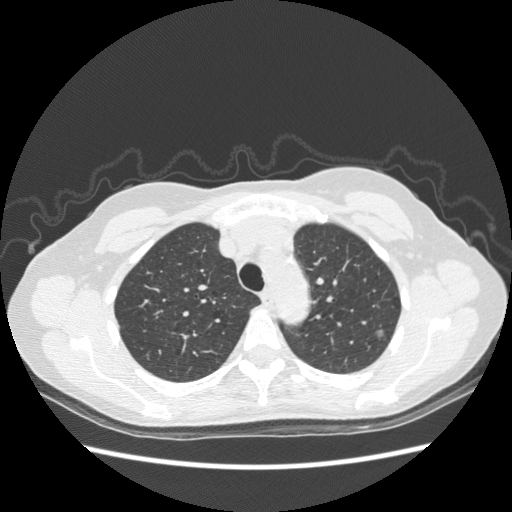
Low-dose screening chest CT, axial slice. First (baseline) screen. Lung window (W 1500 / L -600 HU). 1.25 mm slice thickness. Slice 70 of 270 in the series. Female participant, aged 61 years at enrolment. Former smoker at enrolment.
- Lesion marked by an expert reader, bounding box [x1, y1, x2, y2] px = [358, 320, 390, 350].
- Screening reader's record for this exam (one nodule recorded; not confirmed to be the boxed lesion): non-calcified nodule or mass ≥4 mm, left upper lobe, 7 × 6 mm, poorly defined margins, ground glass attenuation.
- Official screen result: positive, change unspecified: nodule(s) >= 4 mm or enlarging nodule(s), mass(es), or other non-specific abnormalities suspicious for lung cancer.
- Lung cancer was diagnosed 484 days after this screen (after the second annual screen): bronchiolo-alveolar adenocarcinoma, NOS, left upper lobe, well differentiated (G1), stage IA (AJCC 6th edition), 8 mm at pathology.